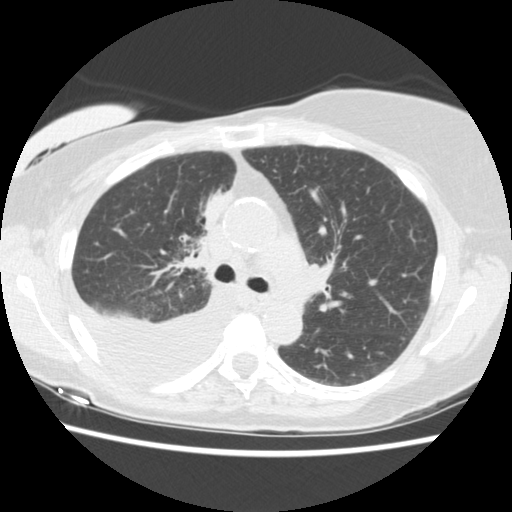
Chest CT (low-dose screening protocol), one axial image; third annual screen; lung window (W 1500 / L -600 HU); 2.5 mm slice thickness; 120 kVp; slice 61 of 157 in the series; 512 × 512 image matrix. Female, age 56 years at enrolment.
Lesion marked by an expert reader, bounding box (x1, y1, x2, y2) in pixels: (182, 183, 242, 249). The screening reader recorded 2 non-calcified nodules or masses ≥4 mm on this exam (right middle lobe, right lower lobe); which of them this box marks is not recorded. Lung cancer was diagnosed 160 days after this screen: adenocarcinoma, NOS, right upper lobe, stage IIIB (AJCC 6th edition), 8 mm at pathology.